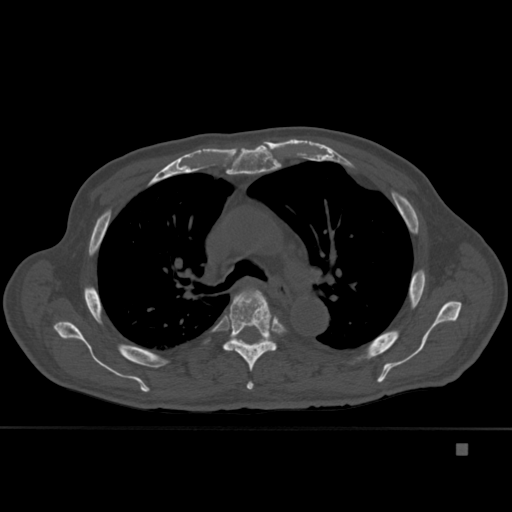
CT including the spine, one axial slice; position 308 of 451 along the scan axis; bone window (W 1800 / L 400 HU); 1.5 mm slice thickness; 512 × 512 image matrix, field of view 378 × 378 mm. Male patient, age 75 years. From the clinical record (not read from this slice): primary cancer: prostate.
Structures marked on this image (semi-automatic segmentation, software-assisted and operator-edited):
- T4 vertebra: box from (x=237, y=290) to (x=254, y=390) px
- T5 vertebra: (x=223, y=288)–(x=285, y=371)